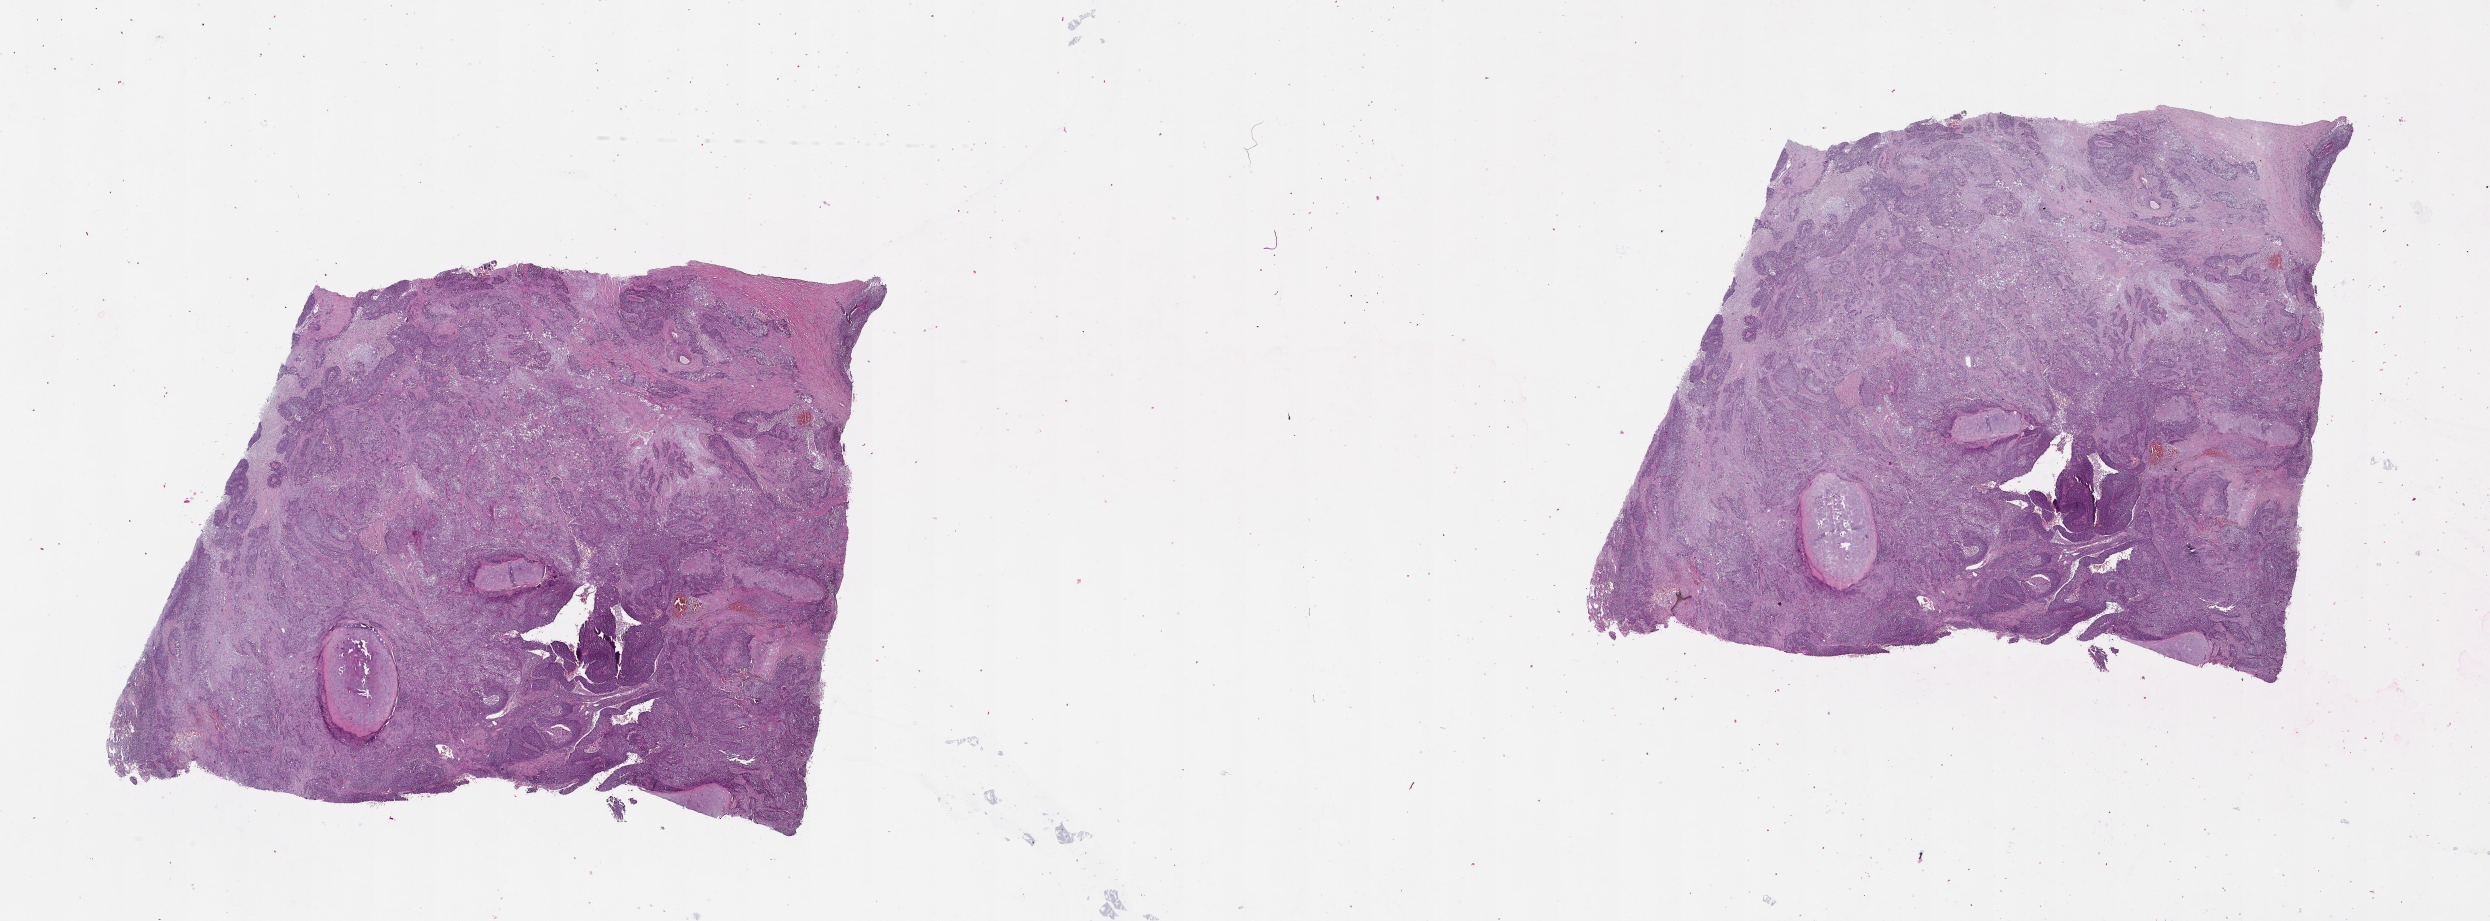
H&E whole-slide image, whole scanned area (about 40.1 x 14.8 mm, acquisition: 20x scan) shown as a low-resolution overview, lung, tumour tissue. 58-year-old male patient.
- patient diagnosis (cohort enrolment): squamous cell carcinoma (lung)